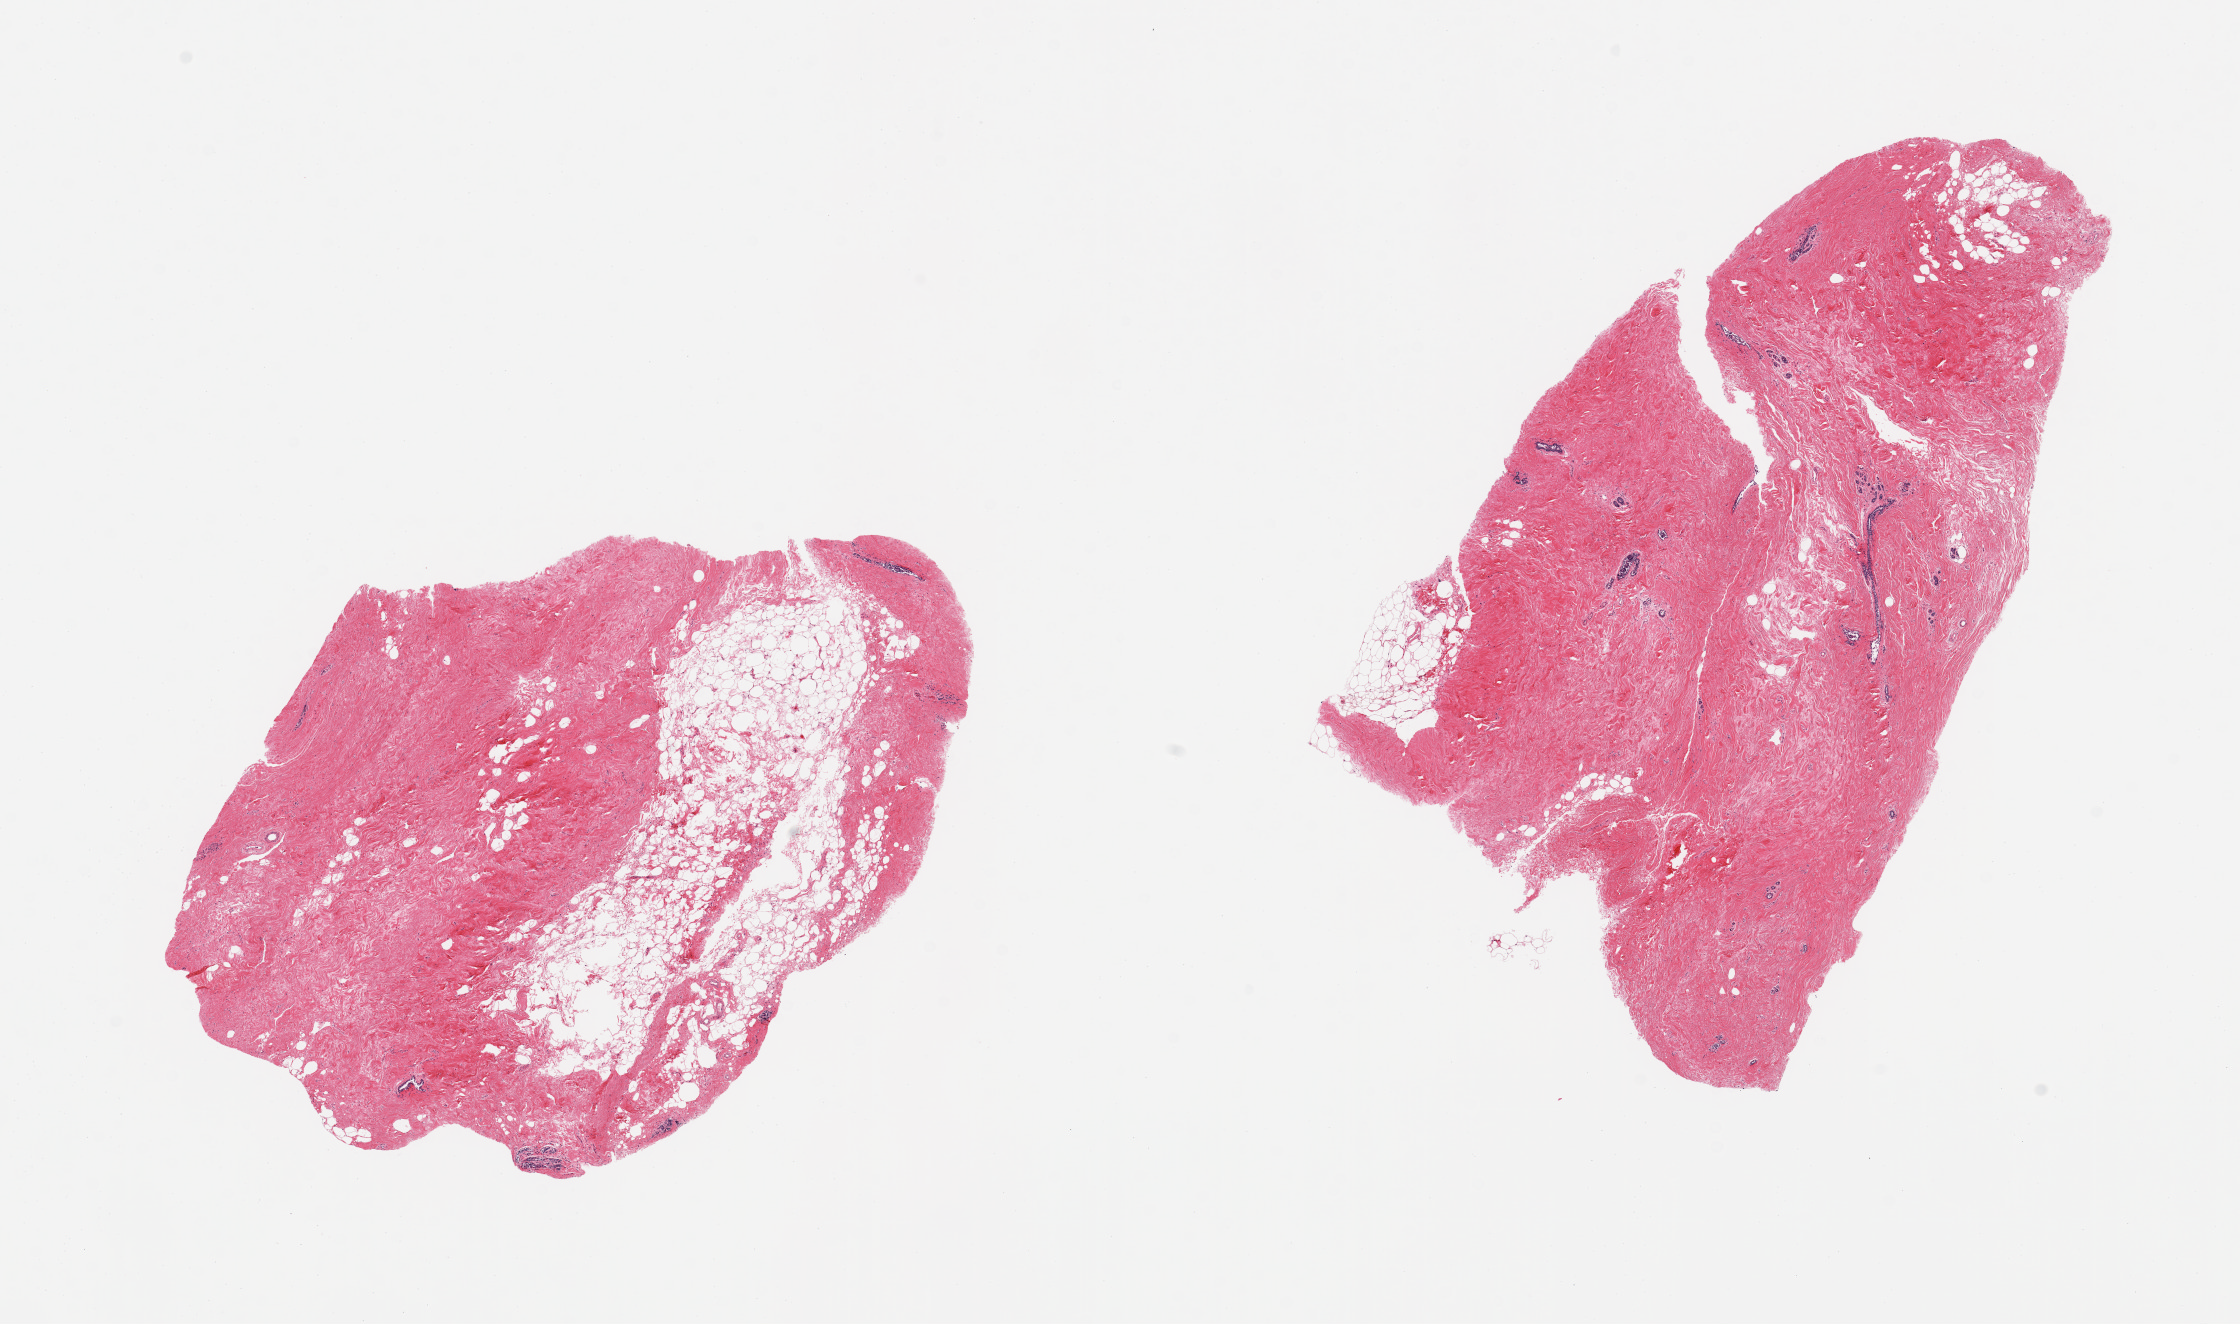
Digitized haematoxylin and eosin-stained section, shown as a low-resolution overview of the whole scanned area (about 17.7 x 10.5 mm, from a 20x scan); PAXgene-fixed paraffin-embedded (PFPE) section; target tissue: breast; donor tissue sample.
Reviewer comment on this tissue sample: 2 pieces; atrophic ductal and lobular units; fibrotic.